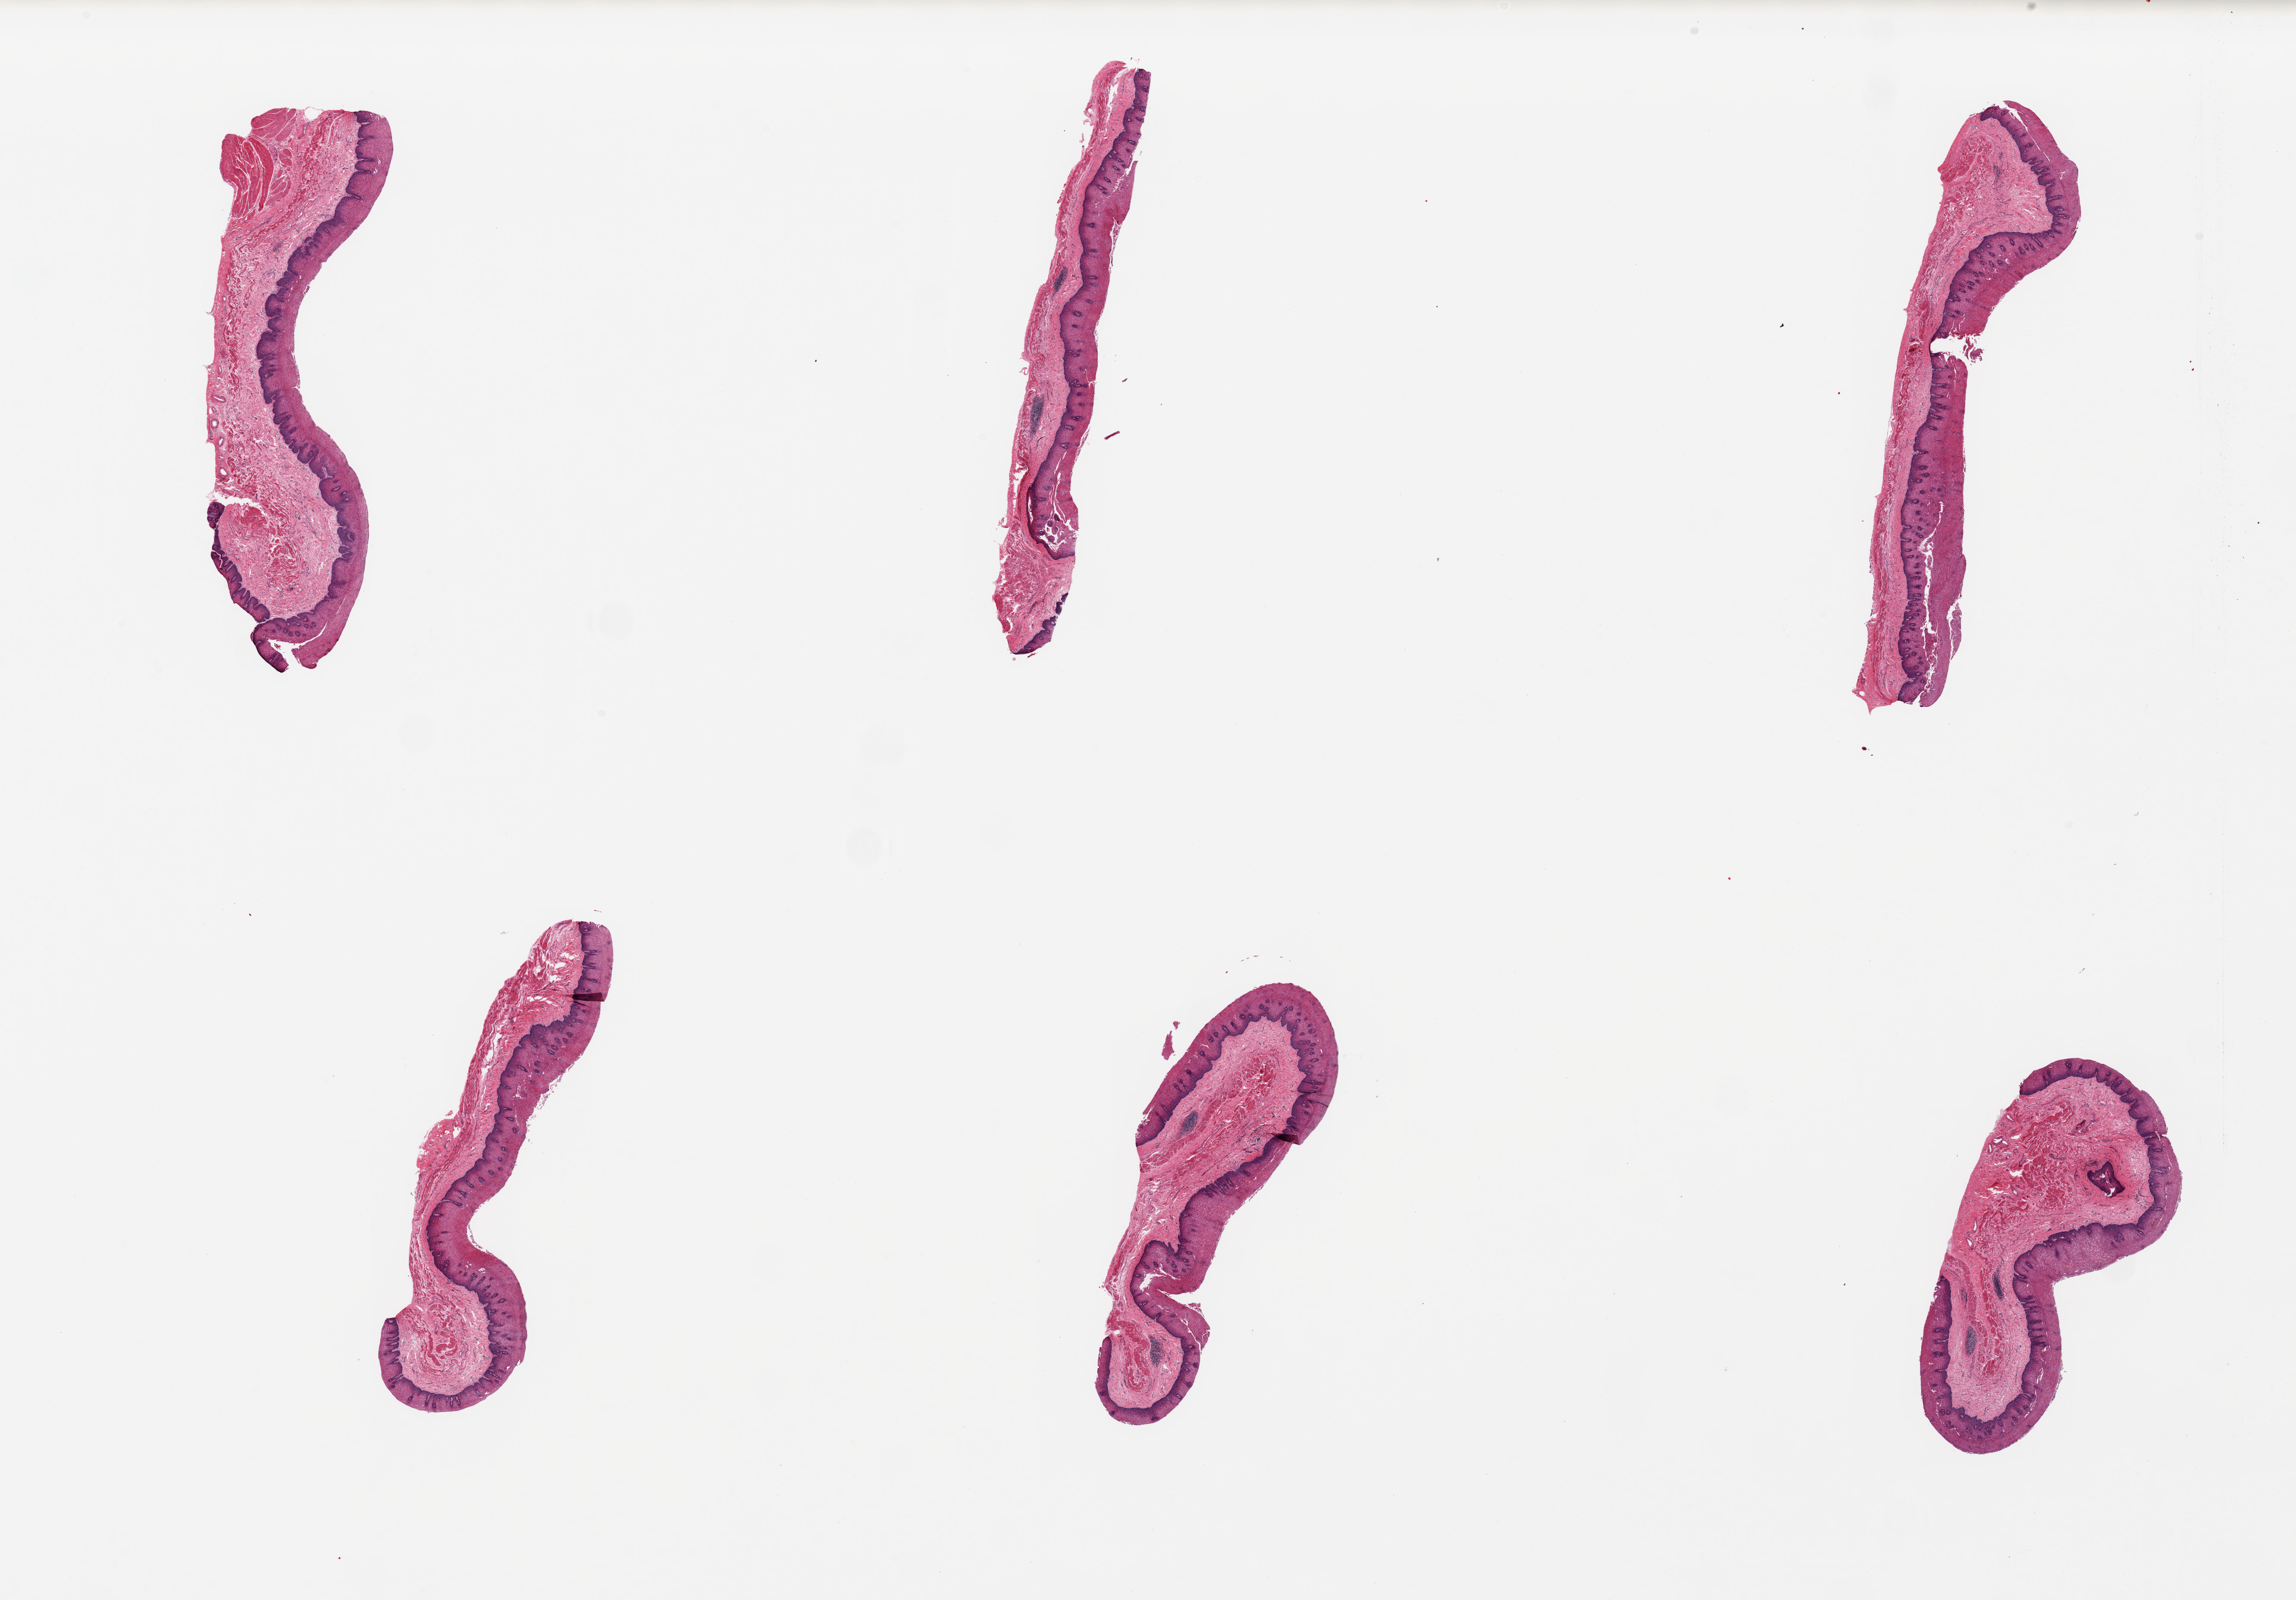
Digitized hematoxylin and eosin (H&E)-stained section — shown as a low-resolution overview of the whole scanned area (about 30.5 x 21.3 mm), PAXgene-fixed paraffin-embedded (PFPE) section, target tissue: esophageal mucous membrane, tissue donor sample.
Pathologist's review note for this sample: 6 pieces, up to 8x2mm; good specimen.